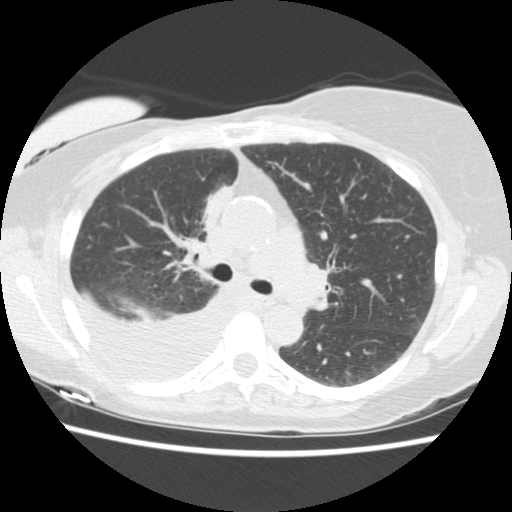
Axial slice from a low-dose chest CT screening exam. Third screening round (two years after baseline). Lung window (W 1500 / L -600 HU). 2.5 mm slice thickness. Standard (soft-tissue) reconstruction kernel (STANDARD). 512 × 512 image matrix, field of view 330 × 330 mm. Female participant, aged 56 years at enrolment.
Expert-annotated lung lesion, bounding box <182,181,243,247> (left, top, right, bottom; pixels). The screening reader recorded 2 non-calcified nodules or masses ≥4 mm on this exam (right middle lobe, right lower lobe); which of them this box marks is not recorded. Official screen result: positive, other. Lung cancer was diagnosed 160 days after this screen: adenocarcinoma, NOS, right upper lobe, stage IIIB (AJCC 6th edition), 8 mm at pathology.